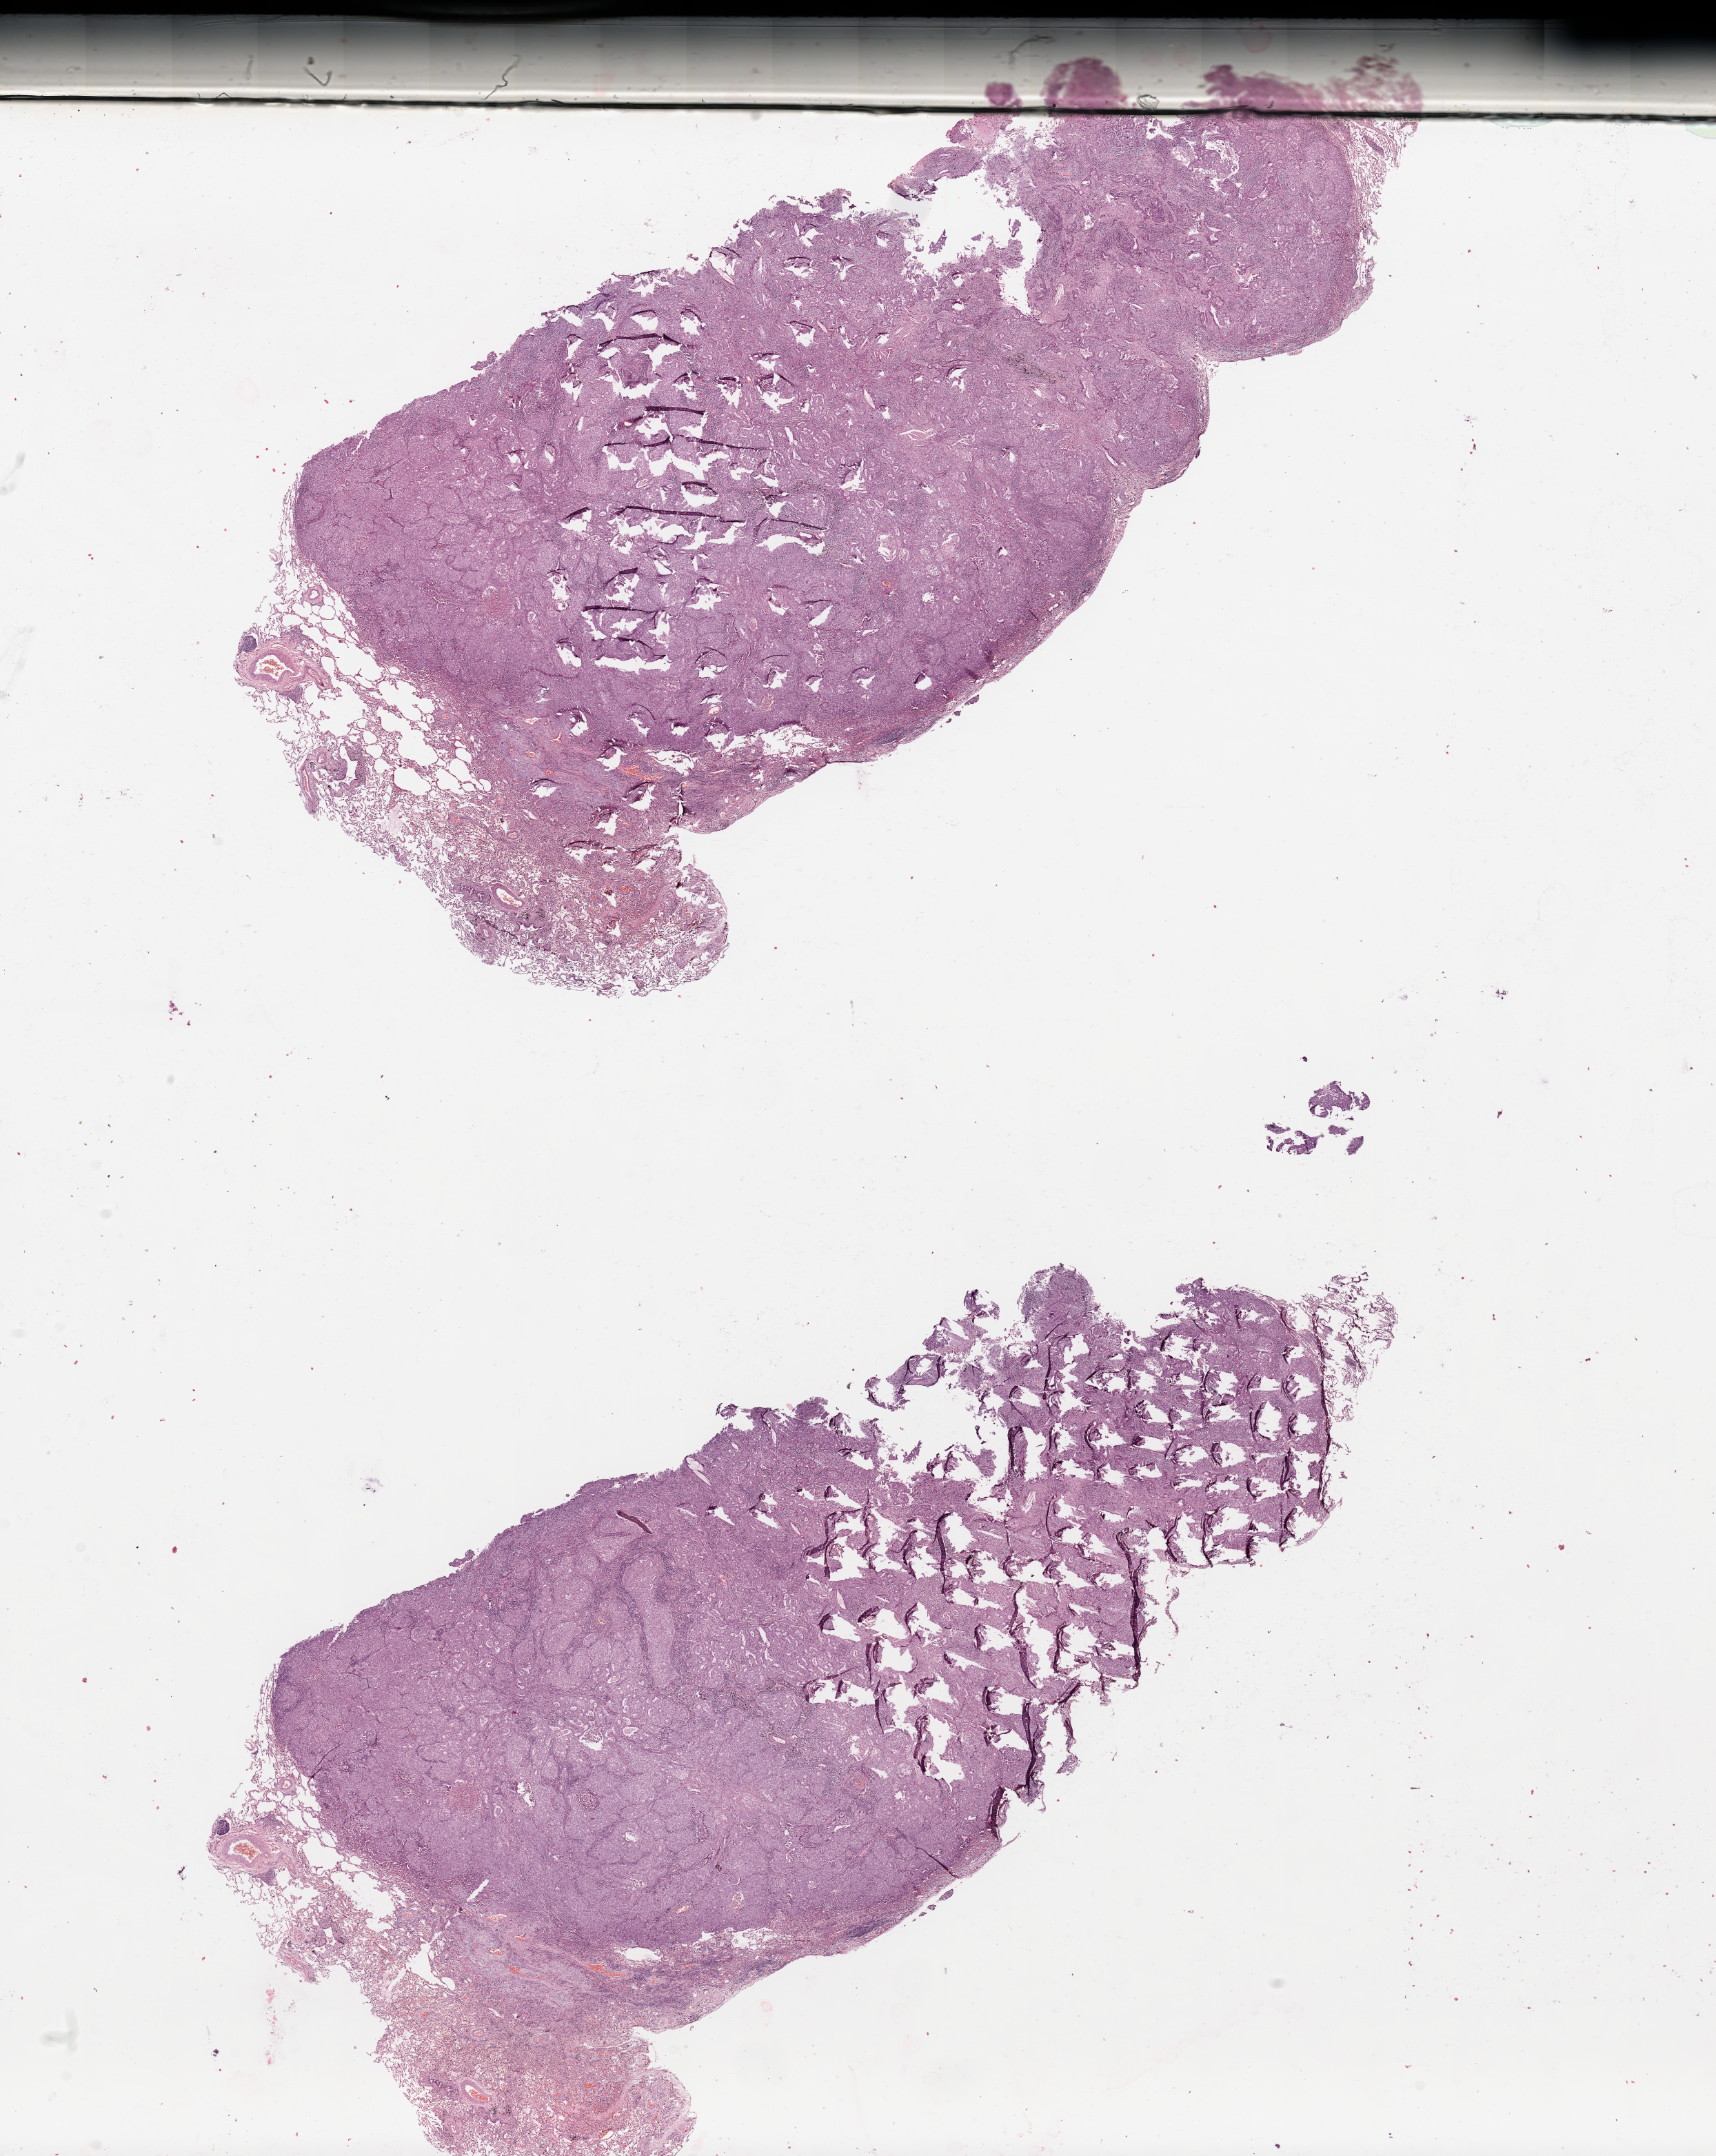
Hematoxylin and eosin (H&E) stained whole-slide image — low-resolution overview of the scanned area, about 19.7 x 24.7 mm (acquisition: 20x scan); tumour tissue sample, lung. Male, 54 y/o. Histologic grade: G2 (moderately differentiated).
• histologic diagnosis: Adenocarcinoma, NOS
• AJCC pathologic stage: IB
• primary tumour site (as recorded): left lower lobe